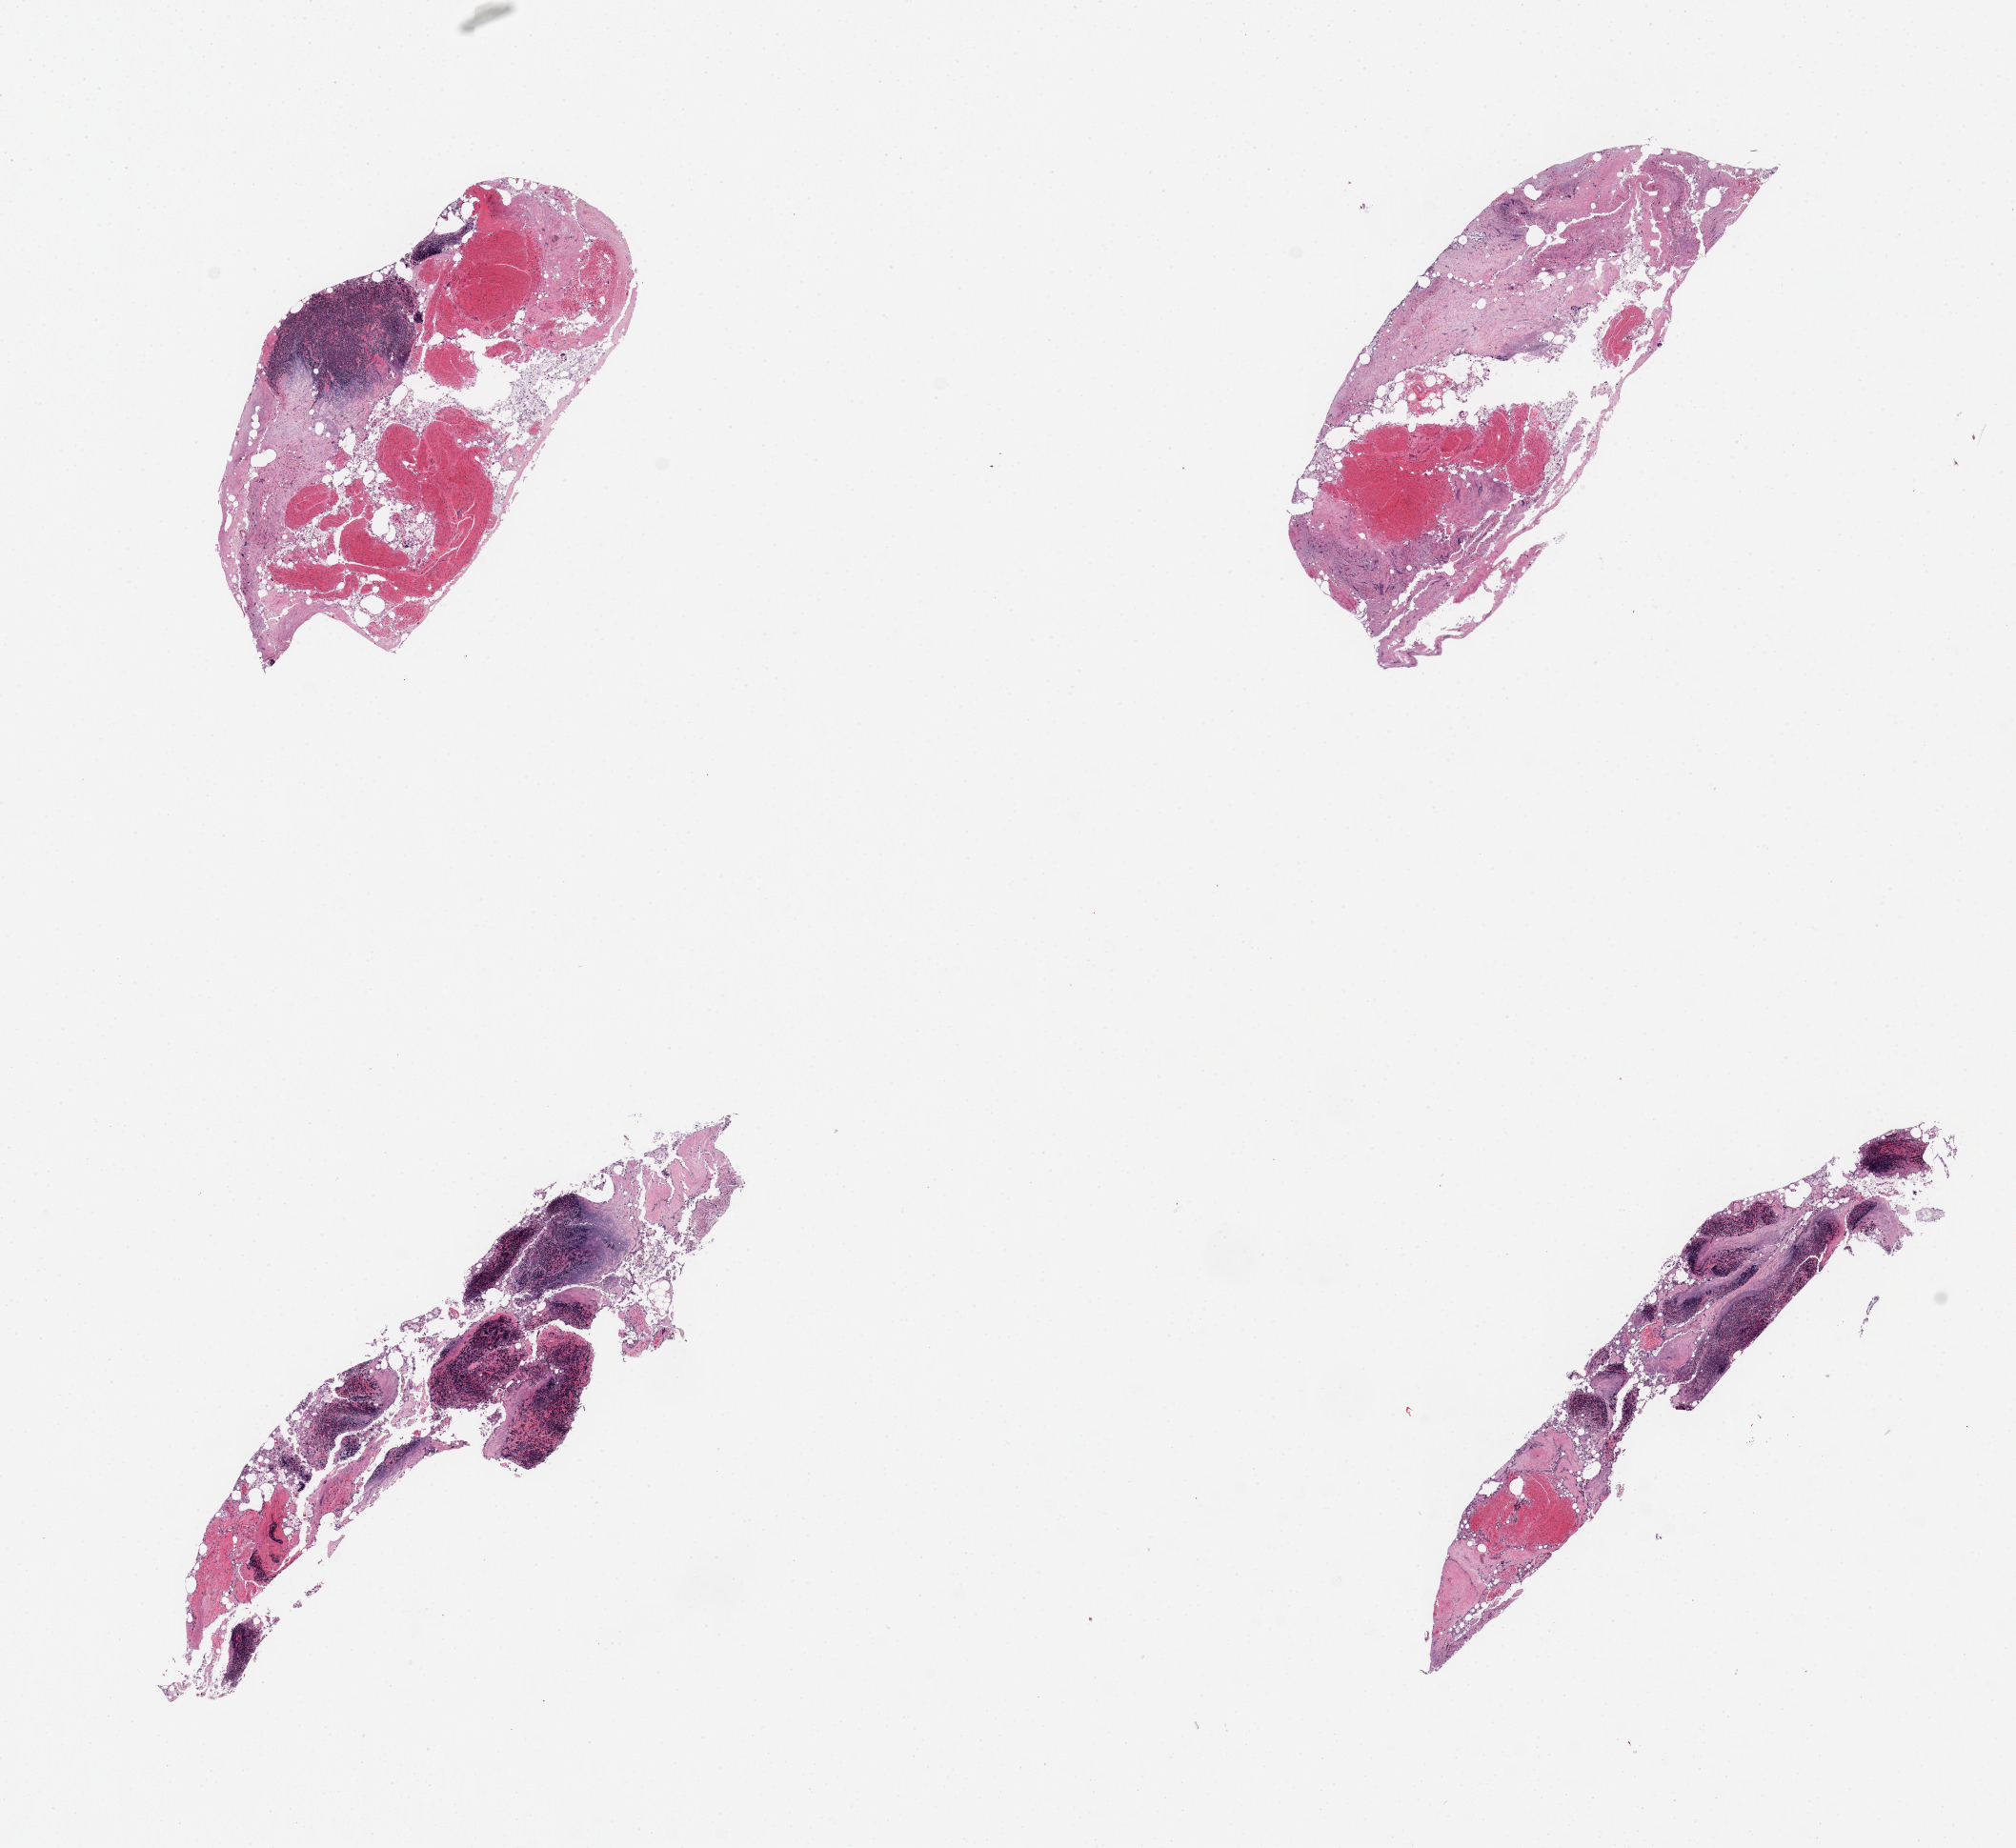
Digitized haematoxylin and eosin-stained section, a low-resolution overview of the entire scanned area, about 16.7 x 15.3 mm. PAXgene-fixed paraffin-embedded (PFPE) section. Section of ileum (target tissue). Tissue donor sample.
Review note (as recorded): 4 pieces, badly autolyzed; ~30% tisssue is lymphoid.